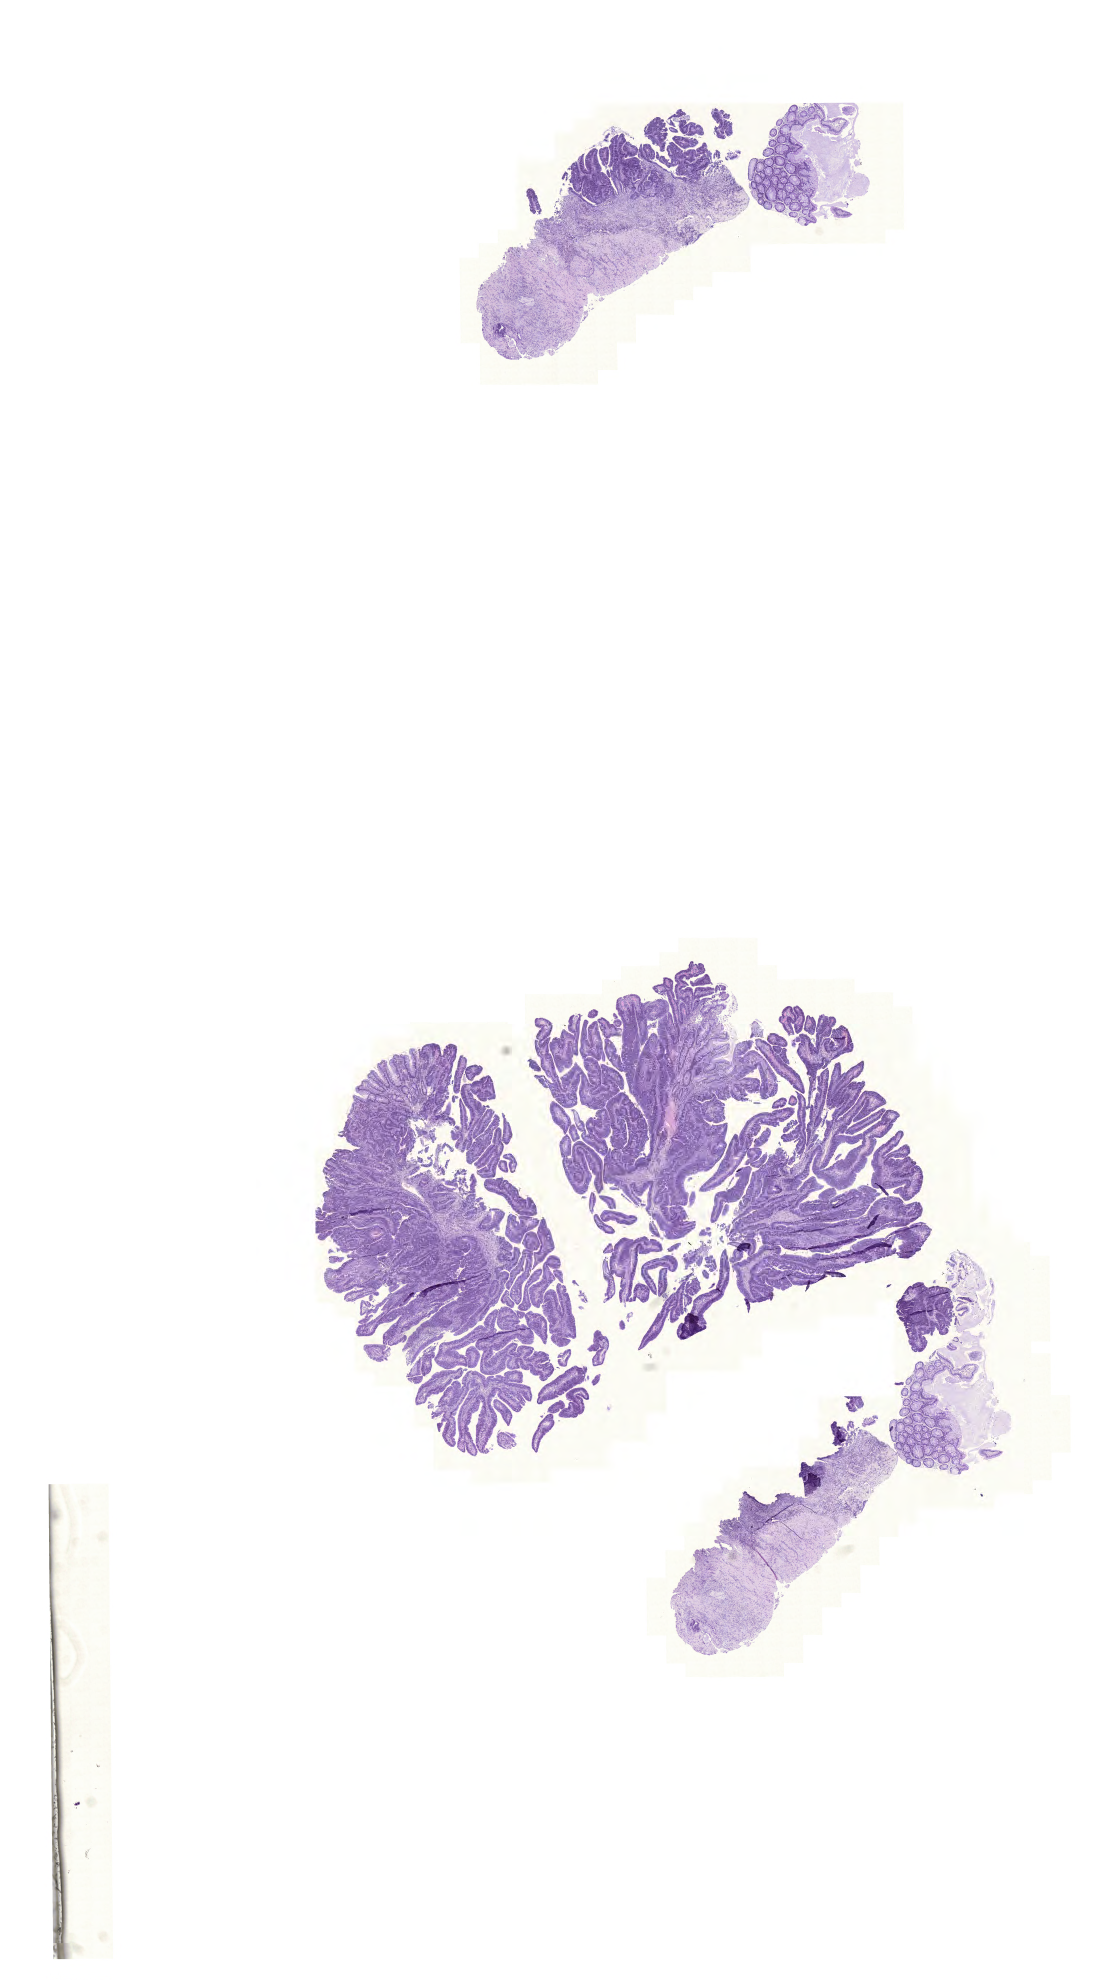
Digitized H&E tissue section (whole slide), a low-resolution overview of the entire scanned area, about 16.5 x 29.5 mm (acquisition: 20x scan). Formalin-fixed paraffin-embedded (FFPE) diagnostic section. Primary tumour sample from the rectum. Male, age 62 years at initial diagnosis.
Lymph nodes positive (case pathology): 31 of 45 examined. Pathologic diagnosis: Adenocarcinoma, NOS (rectosigmoid junction). AJCC pathologic stage: IIIC (6th edition).